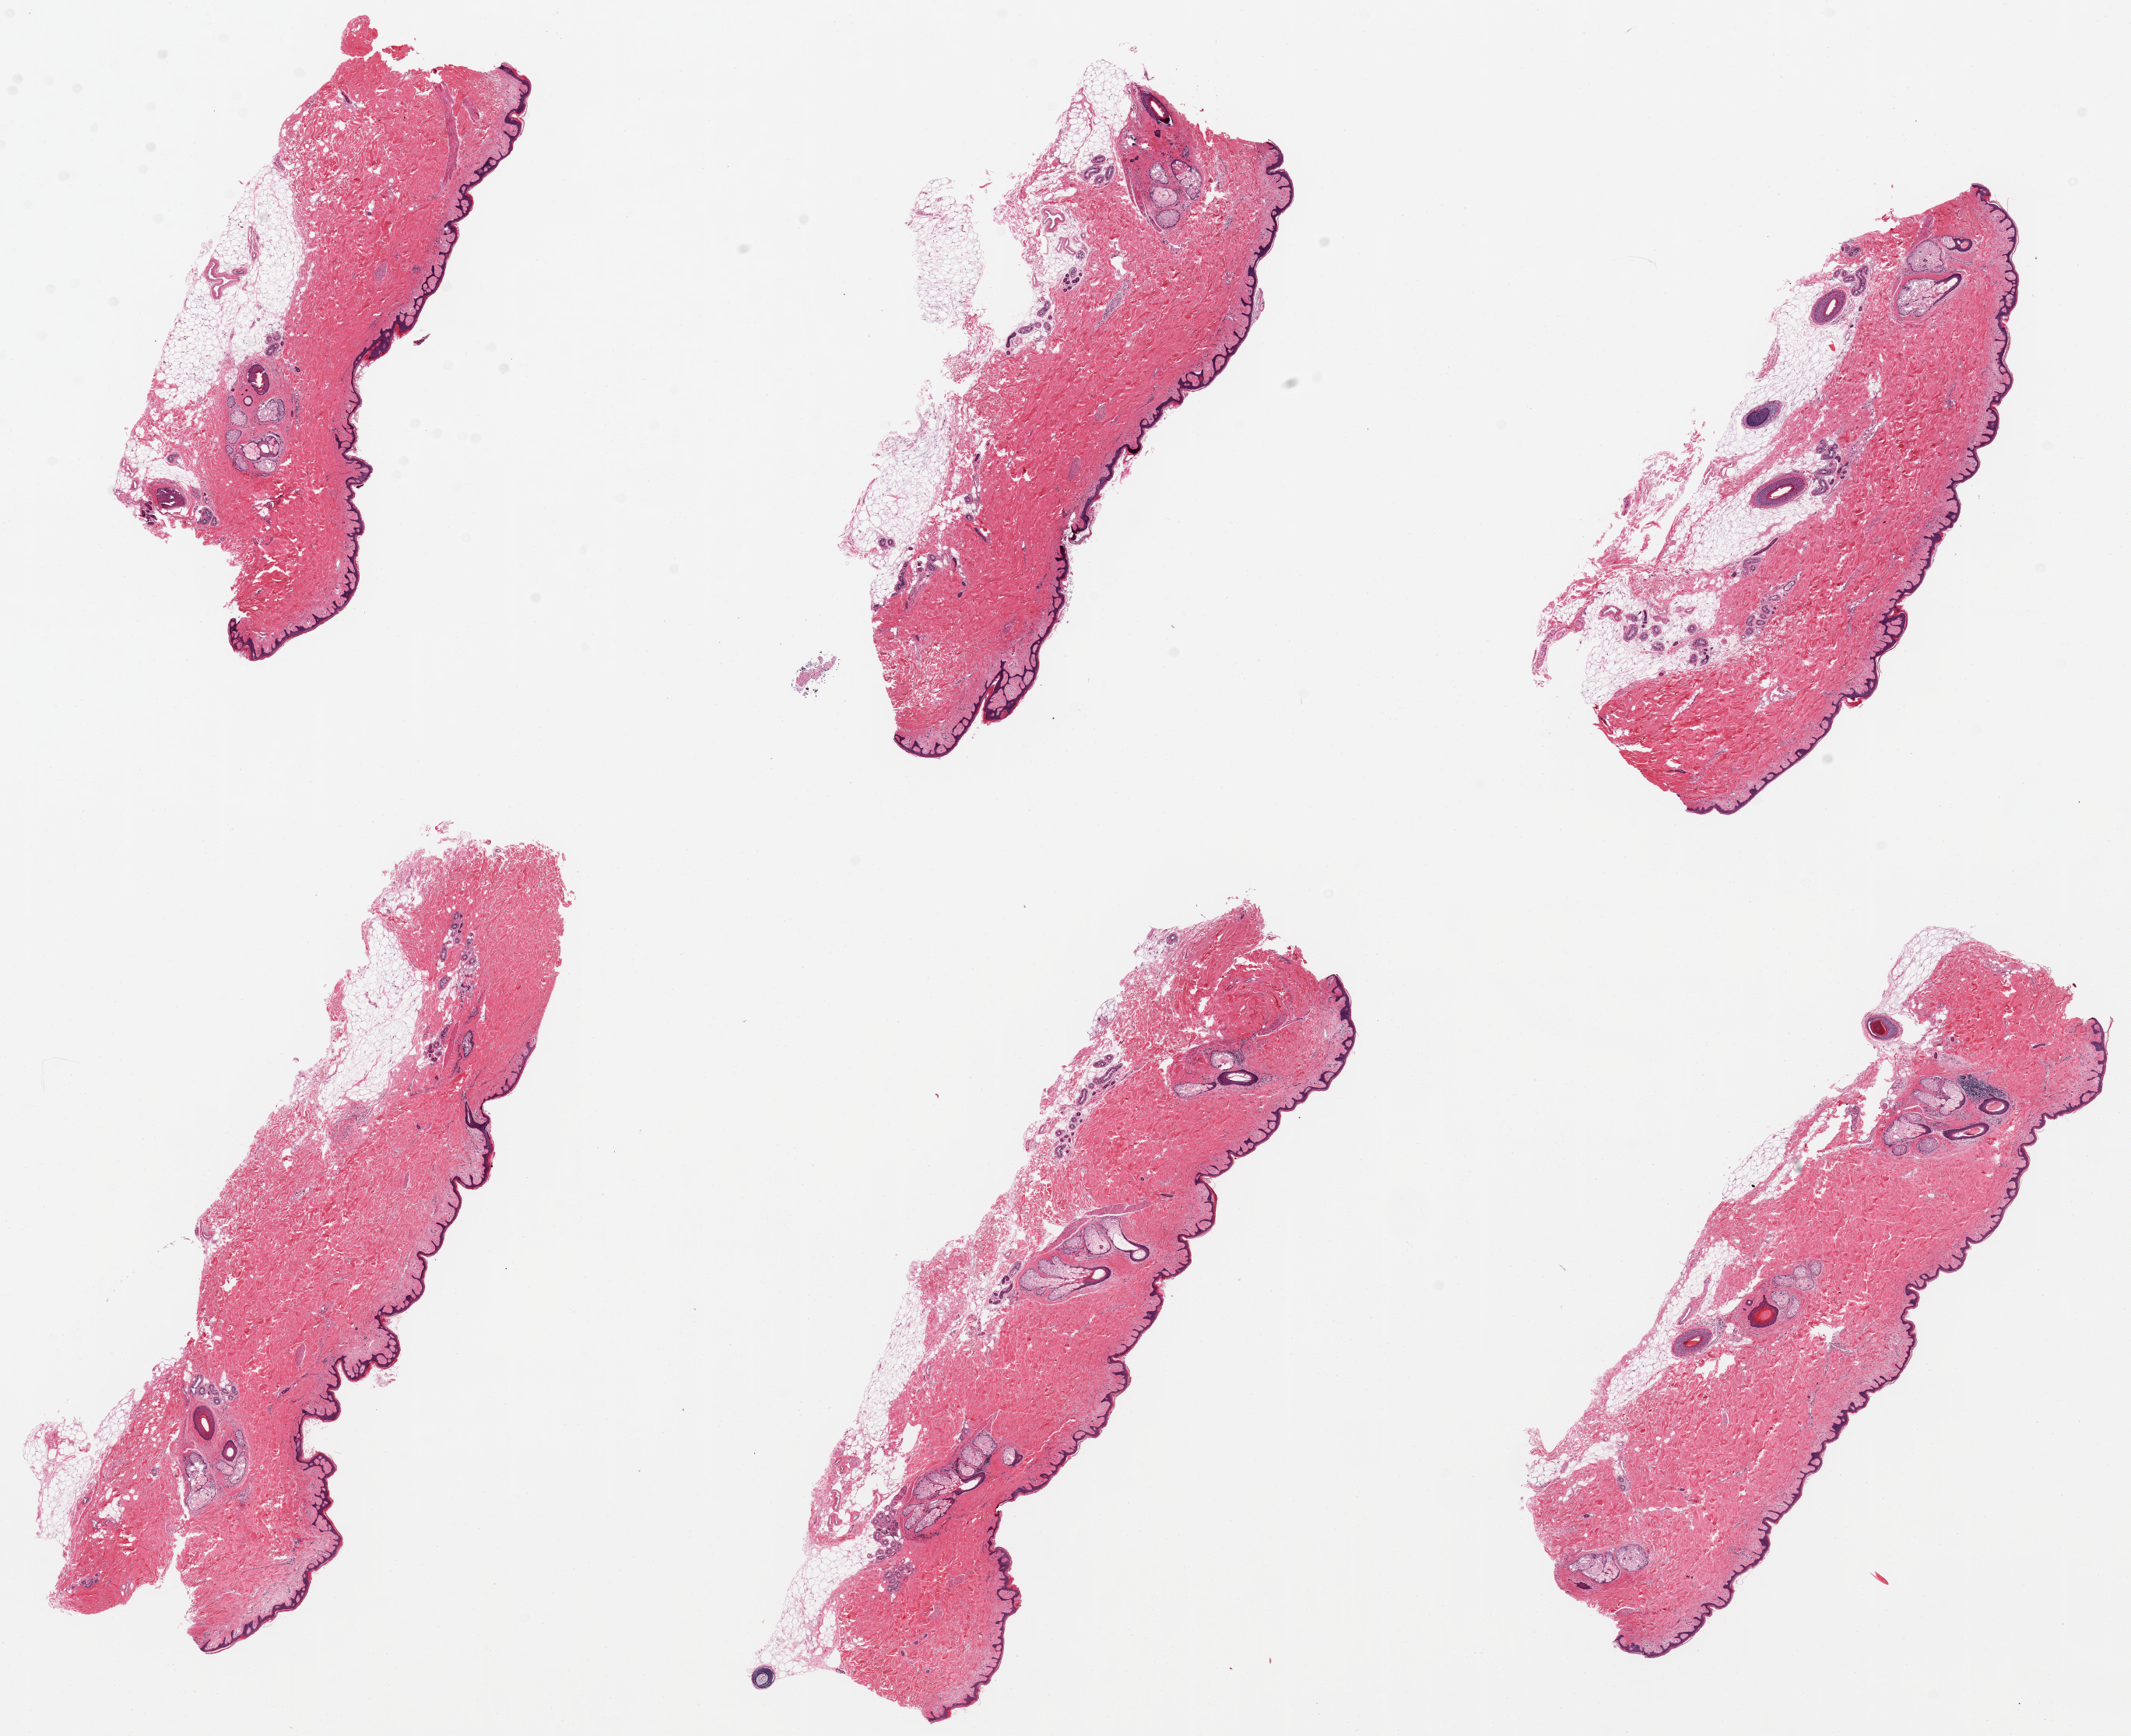
Whole-slide image, haematoxylin and eosin stain — a low-resolution overview of the entire scanned area, about 21.7 x 17.6 mm; PAXgene-fixed paraffin-embedded (PFPE) section; section of skin of suprapubic region (target tissue); tissue donor sample. Donor: female.
- reviewer comment on this tissue sample: 6 pieces, up to 9.5x3mm; up to 1mm subcutaneous adipose